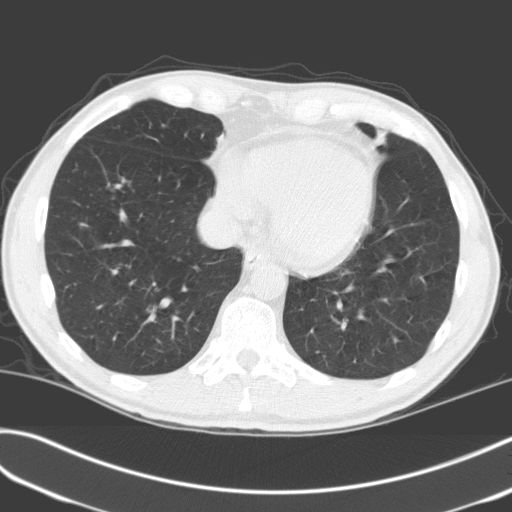
Low-dose screening chest CT, one axial slice. Position 53 of 170 along the scan axis. Lung window (W 1500 / L -600 HU). 3.2 mm slice thickness. 512 × 512 image matrix.
Annotated regions visible in this slice (expert manual segmentation):
- lesion 1 (tumor, upper lobe of left lung): bounding box <373,130,387,146> (left, top, right, bottom; pixels)